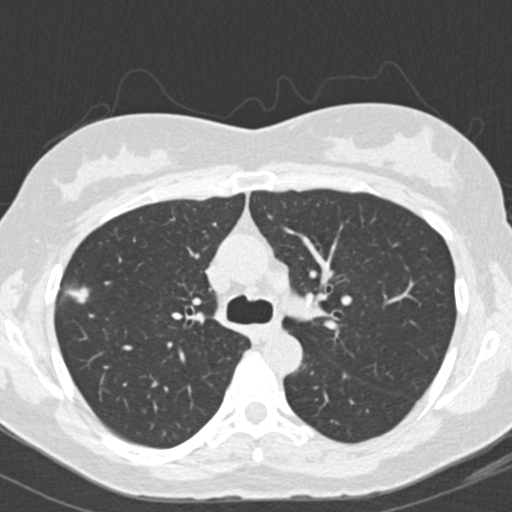
Low-dose screening chest CT, one axial slice; position 110 of 157 along the scan axis; reconstruction kernel B30f; 120 kVp; lung window (W 1500 / L -600 HU); 2 mm slice thickness; 512 × 512 image matrix.
Annotated regions visible in this slice (manually delineated by an expert):
- lesion 1 (tumor, upper lobe of right lung): bounding box <65,287,89,303> (left, top, right, bottom; pixels)